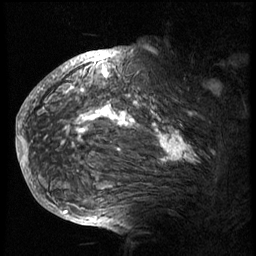
Breast MRI (dynamic contrast-enhanced), one sagittal slice; slice 52 of 74 in the series (ordered by position); 3 images stored at this slice position (order not interpretable as contrast timing); 1.5 T; TE 4.2 ms, TR 8.9 ms; 256 × 256 image matrix, field of view 200 × 200 mm. Female patient, age 57 years. Case-level facts recorded for this patient, not image findings: setting: breast cancer imaged before/during neoadjuvant chemotherapy; receptor status: HER2-positive.
Structures marked on this image (semi-automatic segmentation, software-assisted and operator-edited):
- analysis volume of interest (the breast-tissue region the enhancement analysis was run in; not a lesion): box from (x=40, y=62) to (x=242, y=175) px
- tumour enhancement mask (voxels above the 140 % enhancement threshold inside the analysis volume of interest): (x=44, y=62)–(x=195, y=163)